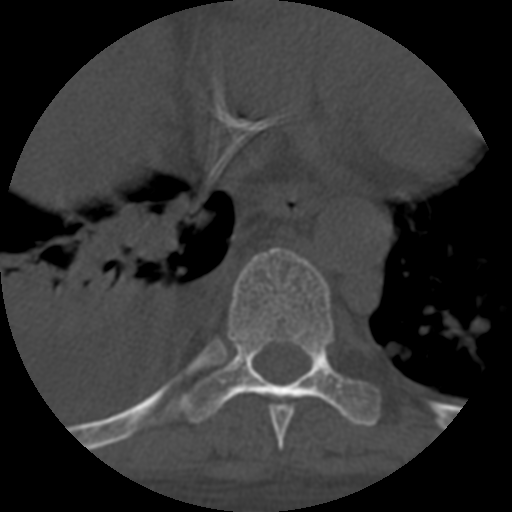
CT including the spine, one axial slice. Position 381 of 708 along the scan axis. Reconstruction kernel STANDARD. 120 kVp. One of 3 acquisitions stored at this slice position. Bone window (W 1800 / L 400 HU). 1.25 mm slice thickness. 512 × 512 image matrix, field of view 160 × 160 mm. Patient age 55 years. Case-level facts recorded for this patient, not image findings: primary cancer: colon; vertebrae with lytic lesions (as recorded): T12, L1, L5.
Annotated regions visible in this slice (semi-automatically segmented with operator editing):
- T8 vertebra: bounding box (x1, y1, x2, y2) in pixels: (269, 405, 294, 450)
- T9 vertebra: (178, 247, 381, 427)